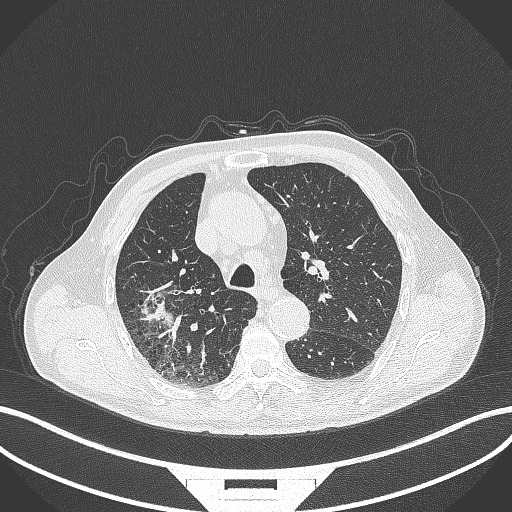
Chest CT, one axial slice; reconstruction kernel B70f; 120 kVp; lung window (W 1500 / L -600 HU); 512 × 512 image matrix. Patient: male, 72 years. Case-level facts recorded for this patient, not image findings: clinical TNM (as recorded): T3 N2 M0.
Annotated regions visible in this slice (bounding box drawn by a radiologist):
- lung tumour (recorded histology: adenocarcinoma): bounding box (x1, y1, x2, y2) in pixels: (134, 283, 186, 337)